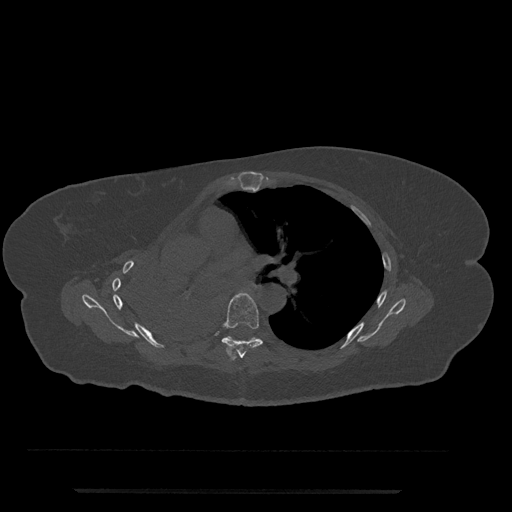
CT including the spine, one axial slice; 120 kVp; bone window (W 1800 / L 400 HU); 512 × 512 image matrix. Female patient, age 51 years. From the clinical record (not read from this slice): primary cancer: neuro.
Annotated regions visible in this slice (semi-automatic segmentation, software-assisted and operator-edited):
- T6 vertebra: box from (x=222, y=293) to (x=263, y=359) px
- T7 vertebra: (x=227, y=336)–(x=256, y=341)